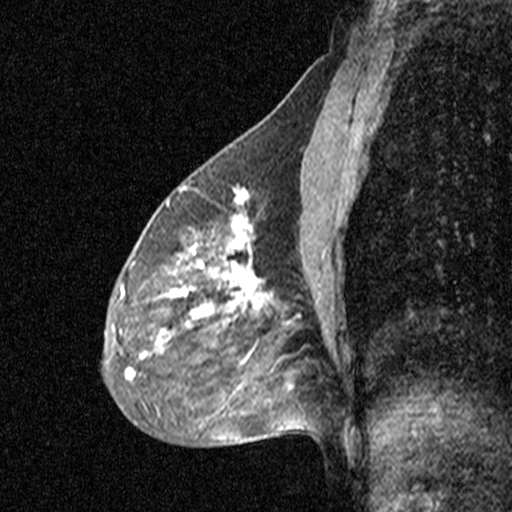
Breast MRI (dynamic contrast-enhanced), one sagittal slice. Position 25 of 44 along the scan axis. Dynamic contrast-enhanced study with each time point stored as its own series, time point 2 of 3 at this slice position (early post-contrast, ordered by acquisition time). 1.5 T. TE 4.5 ms, TR 11 ms. 3 mm slice thickness. 512 × 512 image matrix, field of view 200 × 200 mm. Patient: female, 53 years. Case-level facts recorded for this patient, not image findings: setting: breast cancer imaged before/during neoadjuvant chemotherapy; receptor status: HR-positive, HER2-negative.
Structures marked on this image (semi-automatic segmentation, software-assisted and operator-edited):
- analysis volume of interest (the breast-tissue region the enhancement analysis was run in; not a lesion): bounding box (x1, y1, x2, y2) in pixels: (88, 176, 313, 423)
- tumour enhancement mask (voxels above the 90 % enhancement threshold inside the analysis volume of interest): (104, 191, 300, 380)